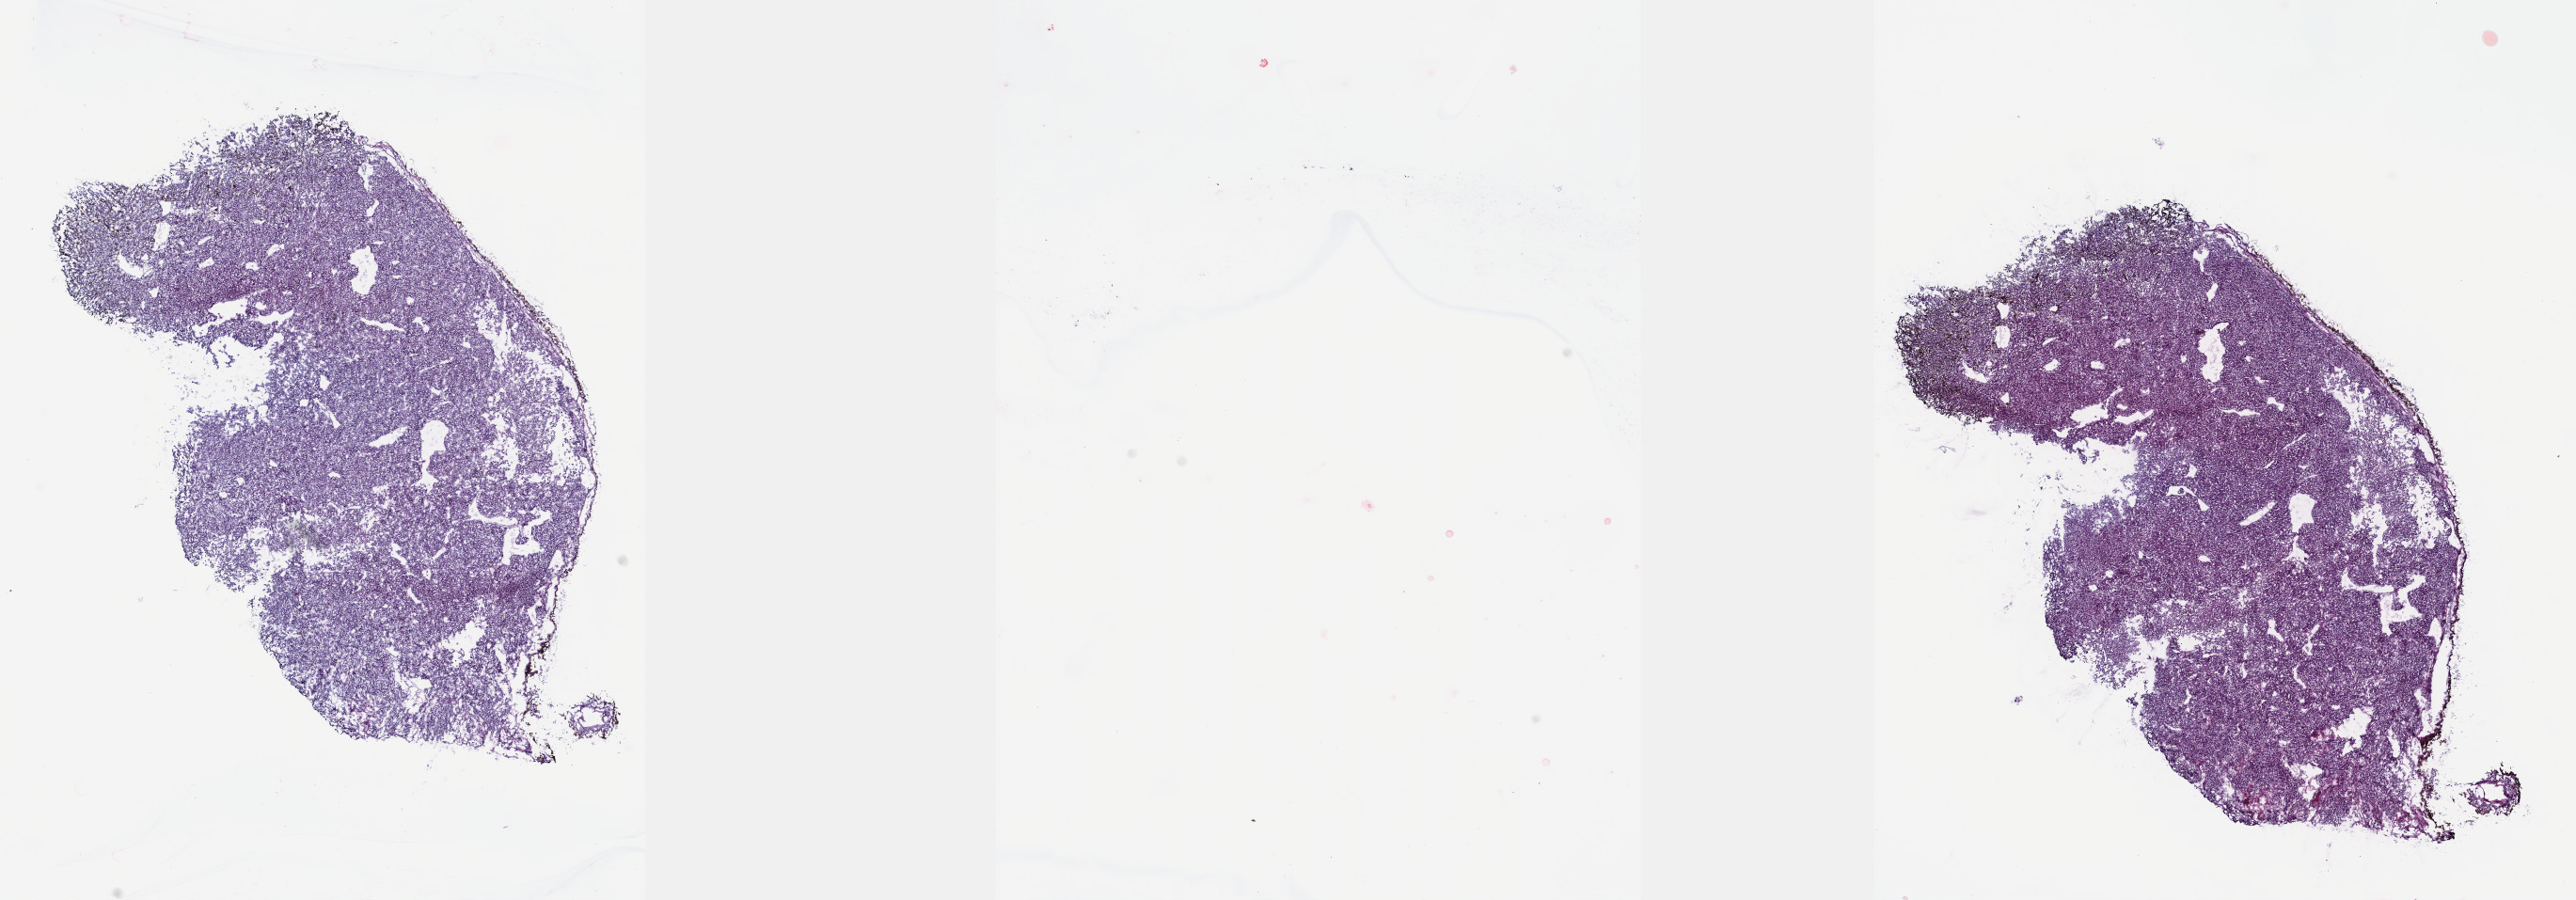
Whole-slide histology image, Hematoxylin and eosin (H&E) stained — whole scanned area (about 22.1 x 7.7 mm) shown as a low-resolution overview; frozen section; uvea, primary tumour sample. Female, age 47 years at initial diagnosis. Pathologist review of this section (percent, as recorded): tumour cells 100%, tumour nuclei 97%, normal cells 0%, stromal cells 0%, necrosis 0%. Infiltration values recorded for this section: lymphocyte infiltration 0%, monocyte infiltration 0%, neutrophil infiltration 0%.
Laterality: right. AJCC pathologic stage: IV (7th edition). Histologic diagnosis: Mixed epithelioid and spindle cell melanoma (overlapping lesion of eye and adnexa). TNM: T4b M1.